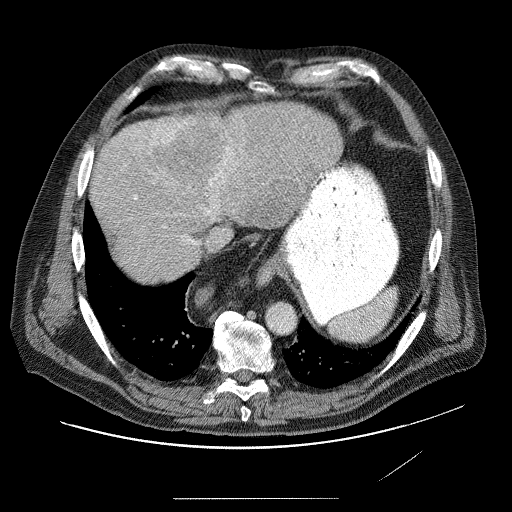
Contrast-enhanced abdominal CT (liver protocol), one axial slice; position 68 of 89 along the scan axis; reconstruction kernel STANDARD; 120 kVp; soft-tissue window (W 400 / L 40 HU); 2.5 mm slice thickness; 512 × 512 image matrix, field of view 420 × 420 mm. From the clinical record (not read from this slice): diagnosis: hepatocellular carcinoma (patient treated with transarterial chemoembolisation; whether this scan precedes or follows treatment is not stated here); TNM stage (as recorded): Stage-IVA; Child-Pugh class: A; tumour differentiation: moderately differentiated.
Annotated regions visible in this slice (semi-automatic segmentation, software-assisted and operator-edited):
- liver parenchyma outside the tumour (the mass and vessels are separate outlines, so this box may not span the whole liver): box from (x=92, y=106) to (x=342, y=266) px
- mass: (x=126, y=111)–(x=303, y=222)
- liver vessels: (x=132, y=188)–(x=243, y=246)